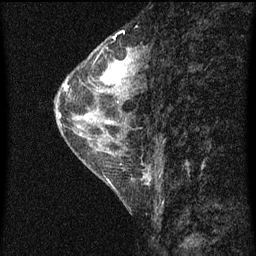
Breast MRI (dynamic contrast-enhanced), one sagittal slice. Slice 26 of 60 in the series (ordered by position). Dynamic contrast-enhanced series, image 2 of 4 at this slice position (ordered by acquisition). 1.5 T. TE 4.2 ms, TR 8 ms. 256 × 256 image matrix. Patient: female, 56 years.
Annotated regions visible in this slice (semi-automatic segmentation, software-assisted and operator-edited):
- analysis volume of interest (the breast-tissue region the enhancement analysis was run in; not a lesion): bounding box <57,54,135,115> (left, top, right, bottom; pixels)
- tumour enhancement mask (voxels above the 70 % enhancement threshold inside the analysis volume of interest): <65,62,130,89>